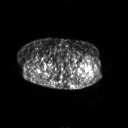
FDG PET of an extremity soft-tissue mass (from a PET/CT study), one axial slice. Slice 259 of 267 in the series (ordered by position). 128 × 128 image matrix, field of view 700 × 700 mm. Female patient, age 62 years. From the clinical record (not read from this slice): histological type: undifferentiated – high grade; grade: high; site of the primary tumour: left thigh.
Outlined on this slice (expert contour drawn on MRI and transferred to this co-registered scan by the dataset authors):
- gross tumour volume including surrounding oedema: bounding box <89,70,93,77> (left, top, right, bottom; pixels)